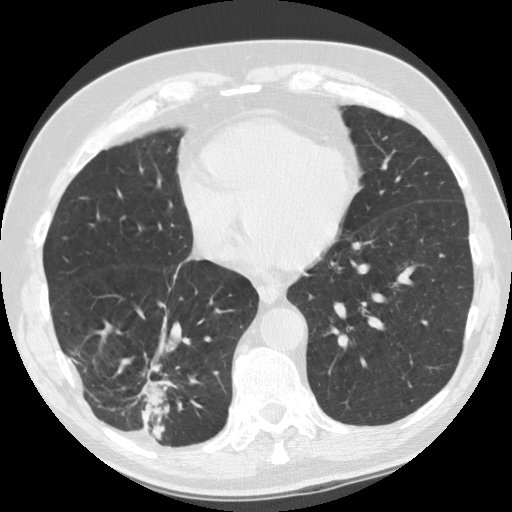
Axial slice from a low-dose chest CT screening exam; baseline screening round; lung window (W 1500 / L -600 HU); standard (soft-tissue) reconstruction kernel (STANDARD). Male participant, aged 69 years at enrolment. Former smoker at enrolment.
Expert reader's lesion annotation, box from (x=100, y=329) to (x=187, y=439) px. The screening reader recorded 2 non-calcified nodules or masses ≥4 mm on this exam (right lower lobe, right lower lobe); which of them this box marks is not recorded. Official screen result: positive, change unspecified: nodule(s) >= 4 mm or enlarging nodule(s), mass(es), or other non-specific abnormalities suspicious for lung cancer. Lung cancer was diagnosed 40 days after this screen: adenocarcinoma, NOS, right lower lobe, stage IIB (AJCC 6th edition), 45 mm at pathology.